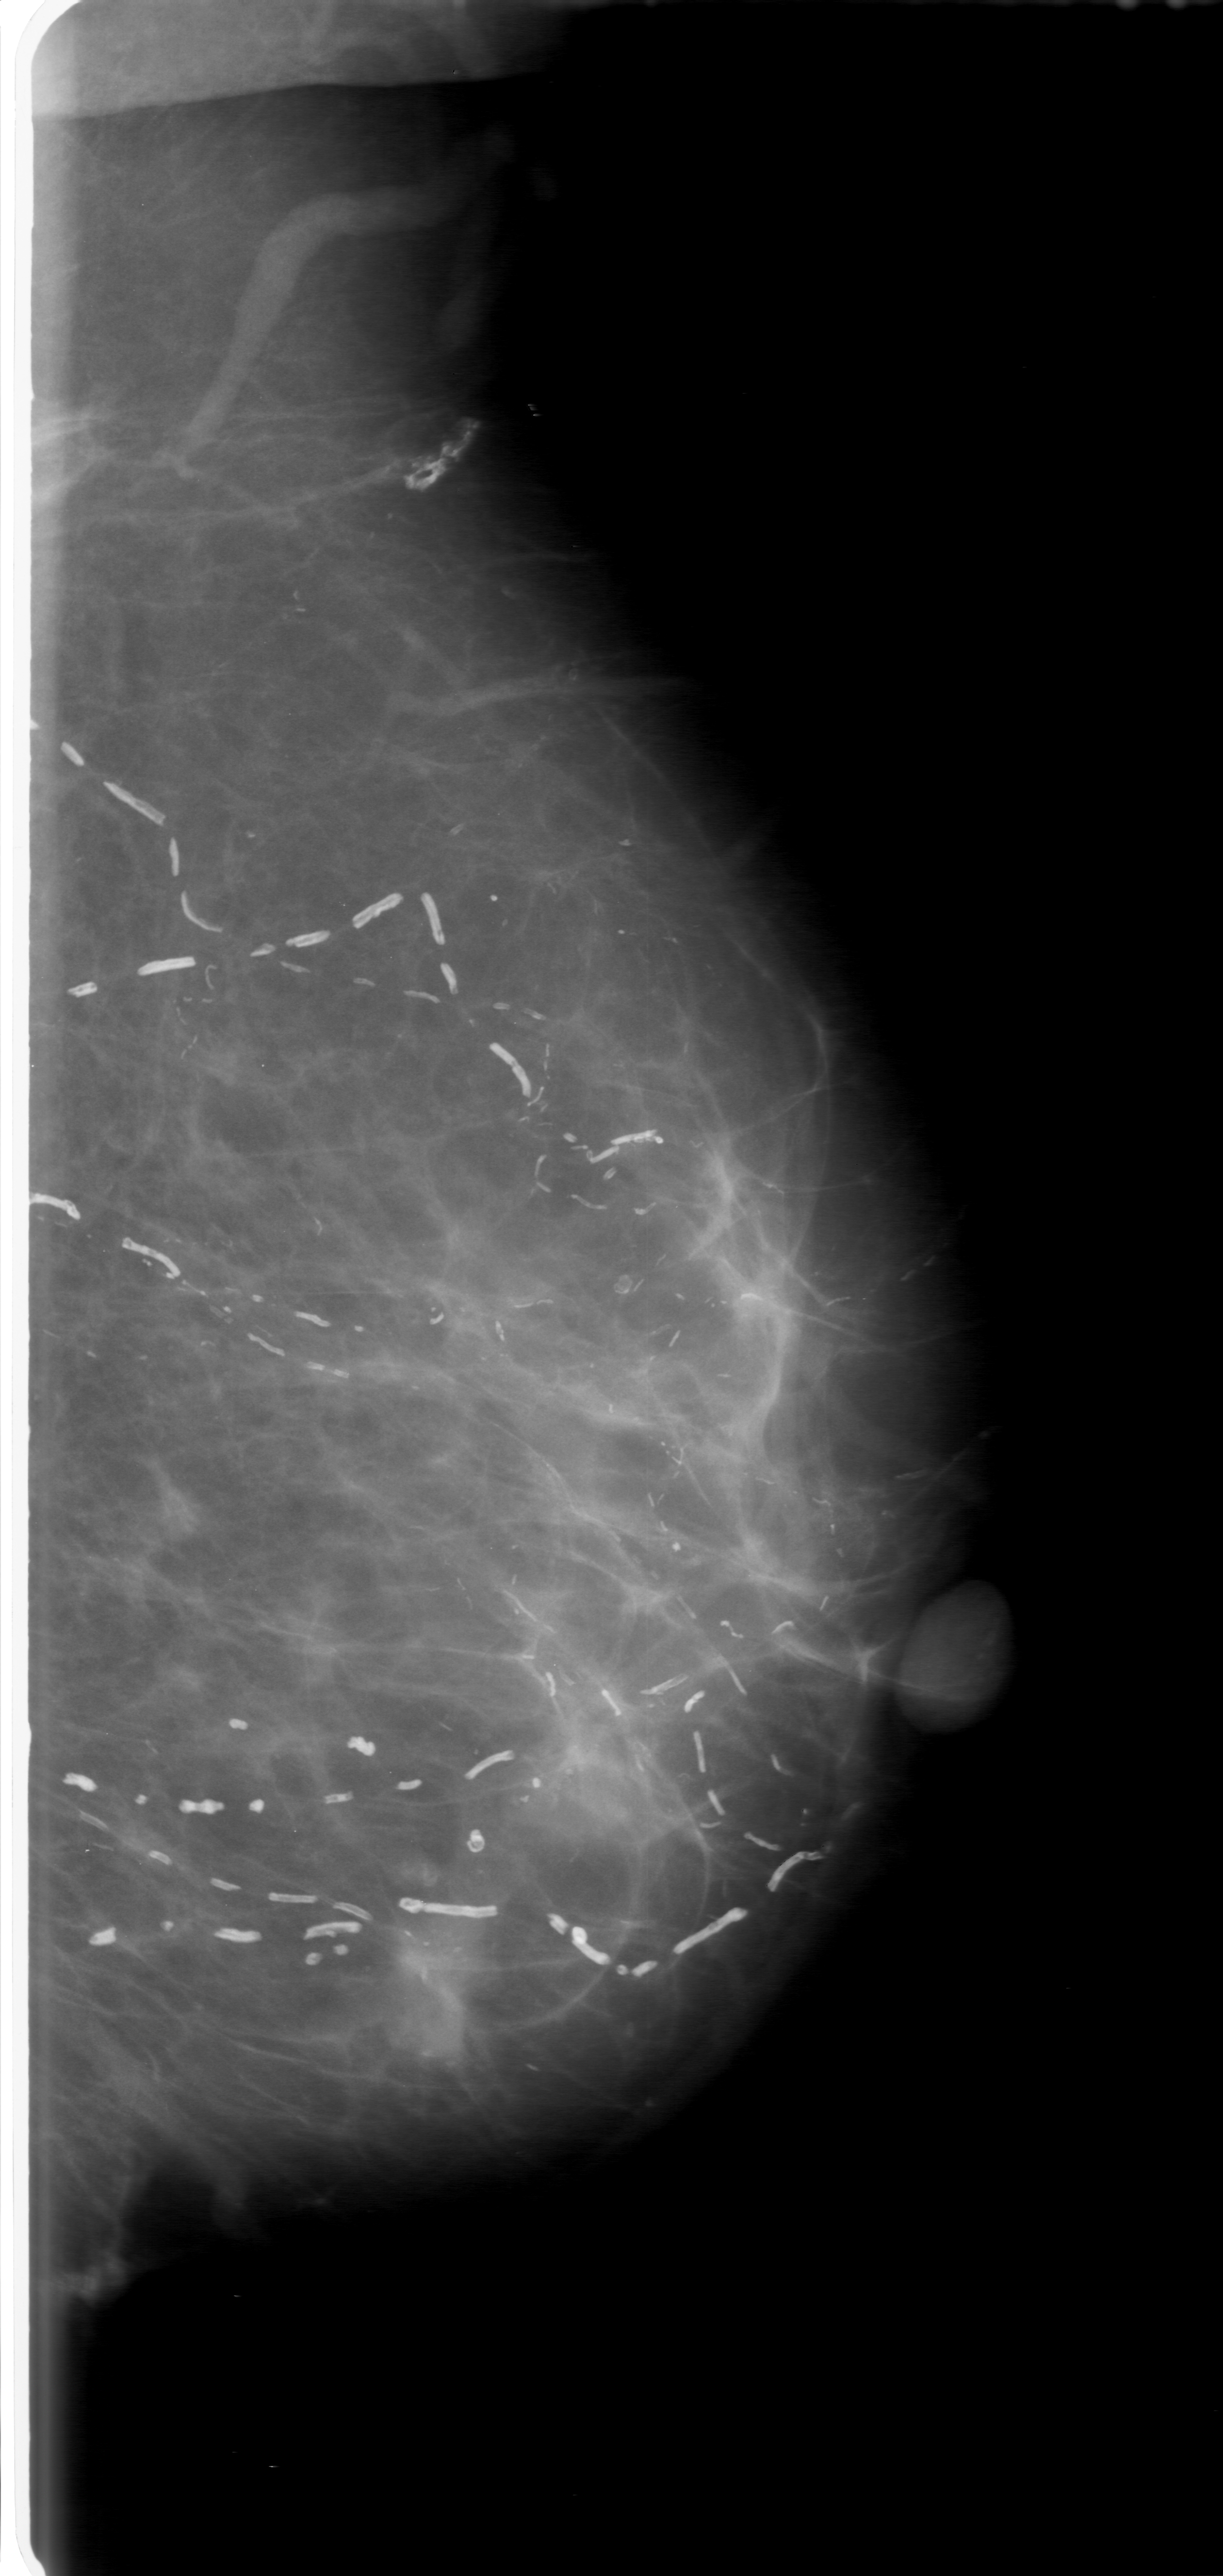
Digitized screen-film mammogram. Left breast. MLO view. Breast composition: scattered fibroglandular densities (BI-RADS density category 2 of 4). 1223 × 2576 image matrix.
Expert-marked regions of interest on this film, with their recorded descriptors:
- mass, shape irregular, margins ill defined; BI-RADS assessment category 3; pathology (as recorded): malignant: bounding box [x1, y1, x2, y2] px = [333, 1900, 530, 2091]